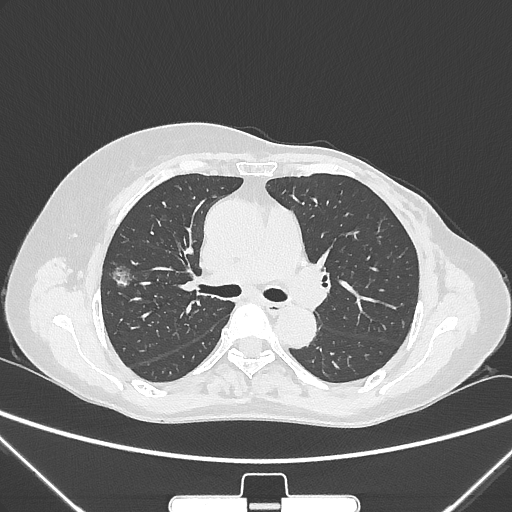
Chest CT, one axial slice. Slice 158 of 265 in the series (ordered by position). Reconstruction kernel IMR1,SharpPlus. 120 kVp. Lung window (W 1500 / L -600 HU). 1 mm slice thickness. 512 × 512 image matrix, field of view 350 × 350 mm. Patient: female, 64 years. From the clinical record (not read from this slice): clinical TNM (as recorded): T1c N0 M0.
Outlined on this slice (bounding box drawn by a radiologist):
- lung tumour (recorded histology: adenocarcinoma): bounding box [x1, y1, x2, y2] px = [107, 257, 135, 296]